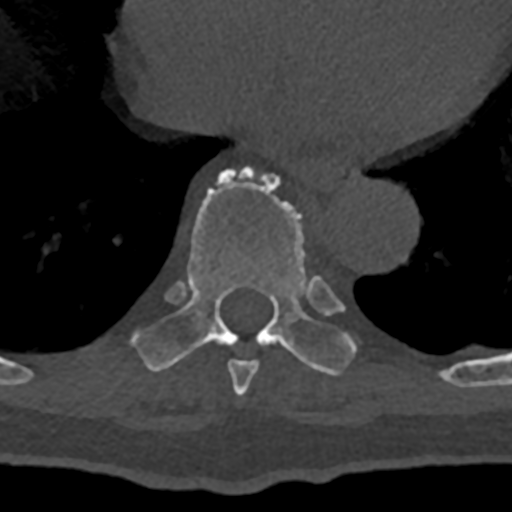
CT including the spine, one axial slice. 120 kVp. Bone window (W 1800 / L 400 HU). 0.5 mm slice thickness. 512 × 512 image matrix, field of view 160 × 160 mm. Male patient, age 74 years. Case-level facts recorded for this patient, not image findings: primary cancer: renal; vertebrae with lytic lesions (as recorded): T10, L1, L2, L3, L4, L5.
Annotated regions visible in this slice (semi-automatically segmented with operator editing):
- T8 vertebra: bounding box <228,359,259,396> (left, top, right, bottom; pixels)
- T9 vertebra: <131,168,357,376>